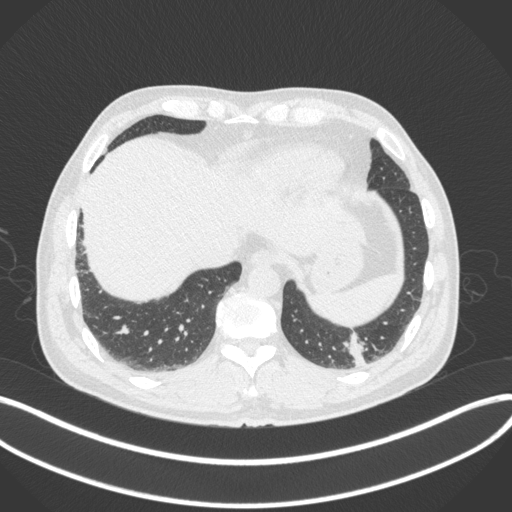
Chest CT, one axial slice; position 54 of 313 along the scan axis; 120 kVp; lung window (W 1500 / L -600 HU); 512 × 512 image matrix, field of view 400 × 400 mm. Male patient, age 54 years. Case-level facts recorded for this patient, not image findings: clinical TNM (as recorded): T1c N0 M1; histopathological grade: G3.
Outlined on this slice (rectangle marked by the reading radiologist):
- lung tumour (recorded histology: adenocarcinoma): box from (x=339, y=333) to (x=372, y=372) px